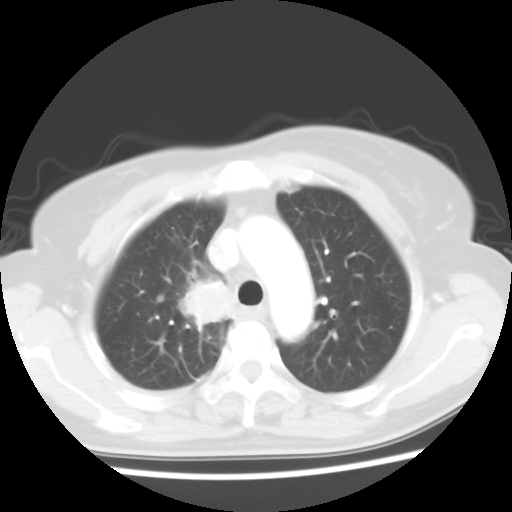
Chest CT, one axial slice. Slice 43 of 56 in the series (ordered by position). 120 kVp. Lung window (W 1500 / L -600 HU). 5 mm slice thickness. 512 × 512 image matrix, field of view 314 × 314 mm. Patient: female, 62 years. Case-level facts recorded for this patient, not image findings: clinical TNM (as recorded): T2 N1 M1a.
Outlined on this slice (bounding box drawn by a radiologist):
- lung tumour (recorded histology: adenocarcinoma): bounding box [x1, y1, x2, y2] px = [169, 273, 234, 337]